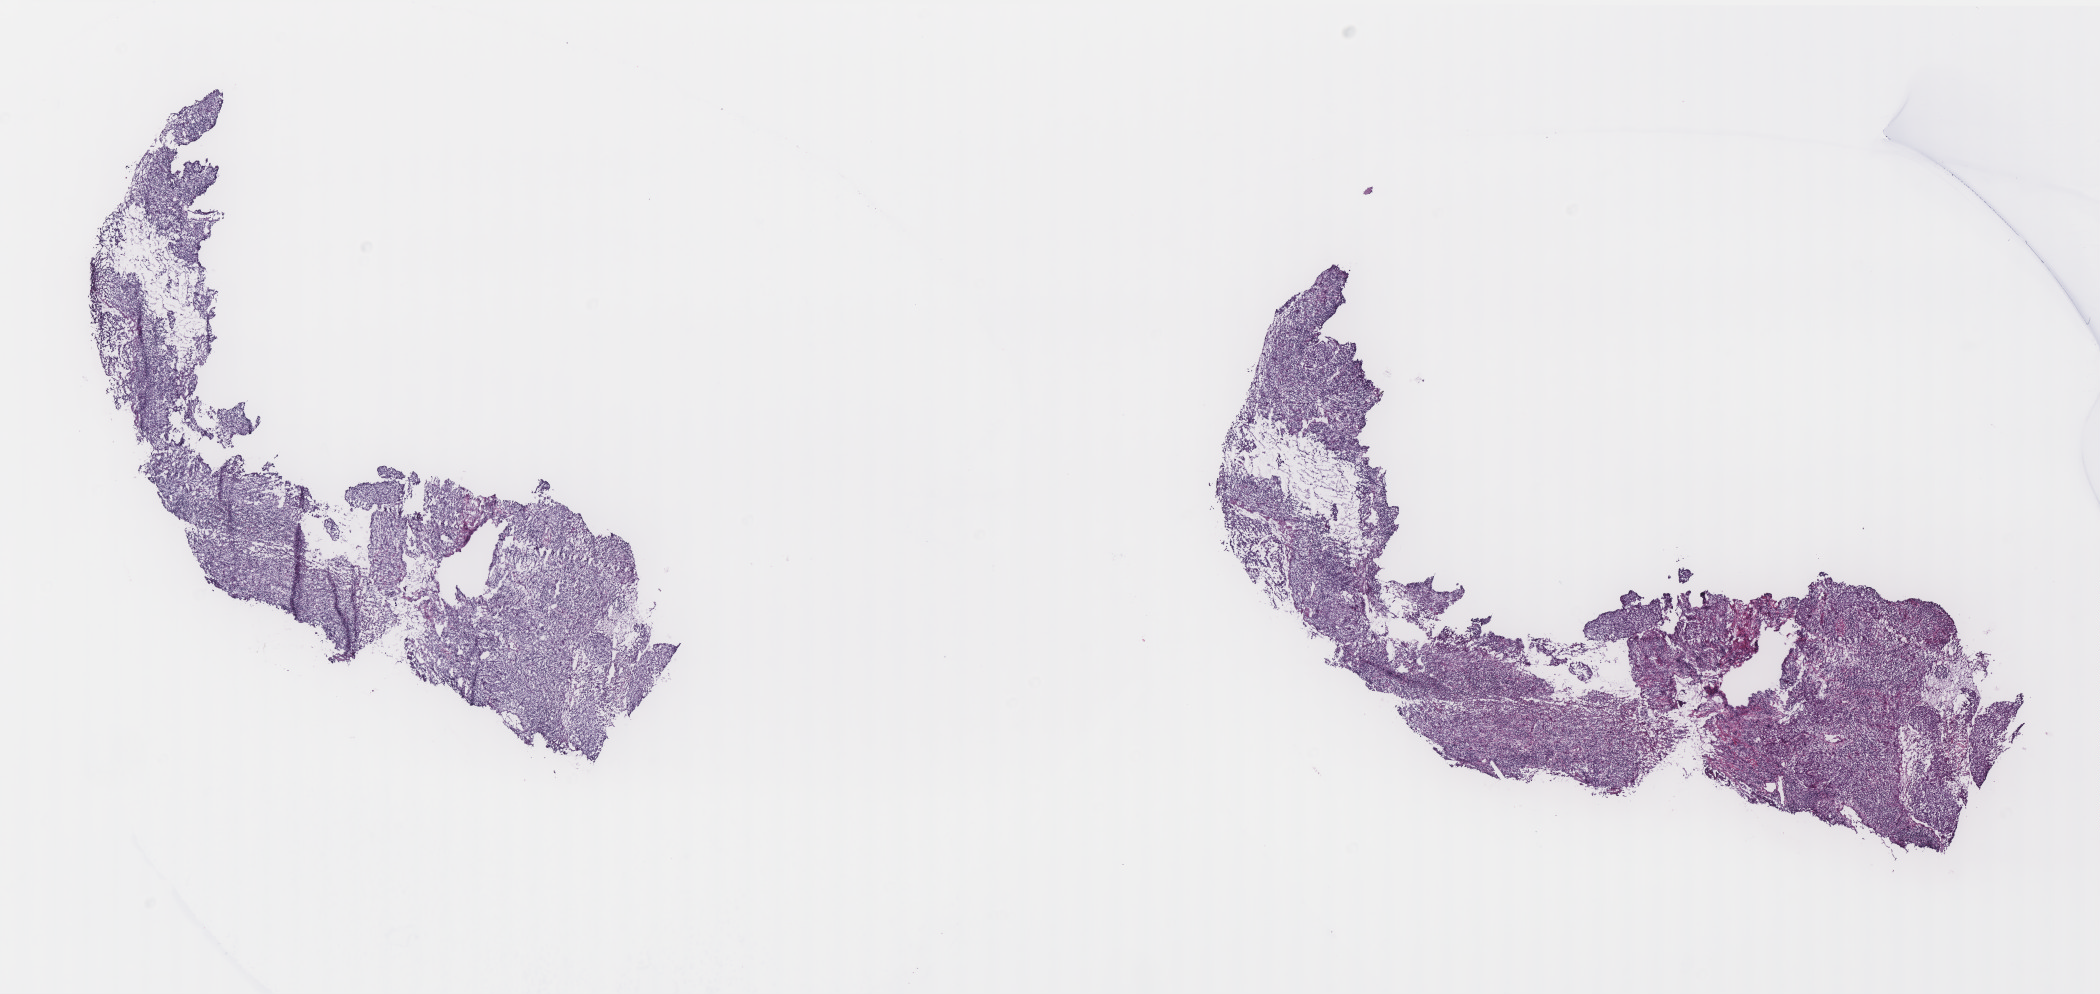
Hematoxylin and eosin (H&E) stained whole-slide image — low-resolution overview of the scanned area, about 16.8 x 8.0 mm (acquisition: 40x scan). Frozen section from the top of the tissue portion. Primary tumour sample from the cervix. Female patient; age at initial diagnosis 31 years. Histologic grade: G2 (moderately differentiated). Pathologist review of this section (percent, as recorded): tumour cells 90%, tumour nuclei 90%, normal cells 0%, stromal cells 10%, necrosis 0%. Inflammatory infiltration, as recorded: lymphocyte infiltration 45%, monocyte infiltration 0%, neutrophil infiltration 5%.
- FIGO stage: IIIB
- pathologic diagnosis: Squamous cell carcinoma, NOS (cervix uteri)